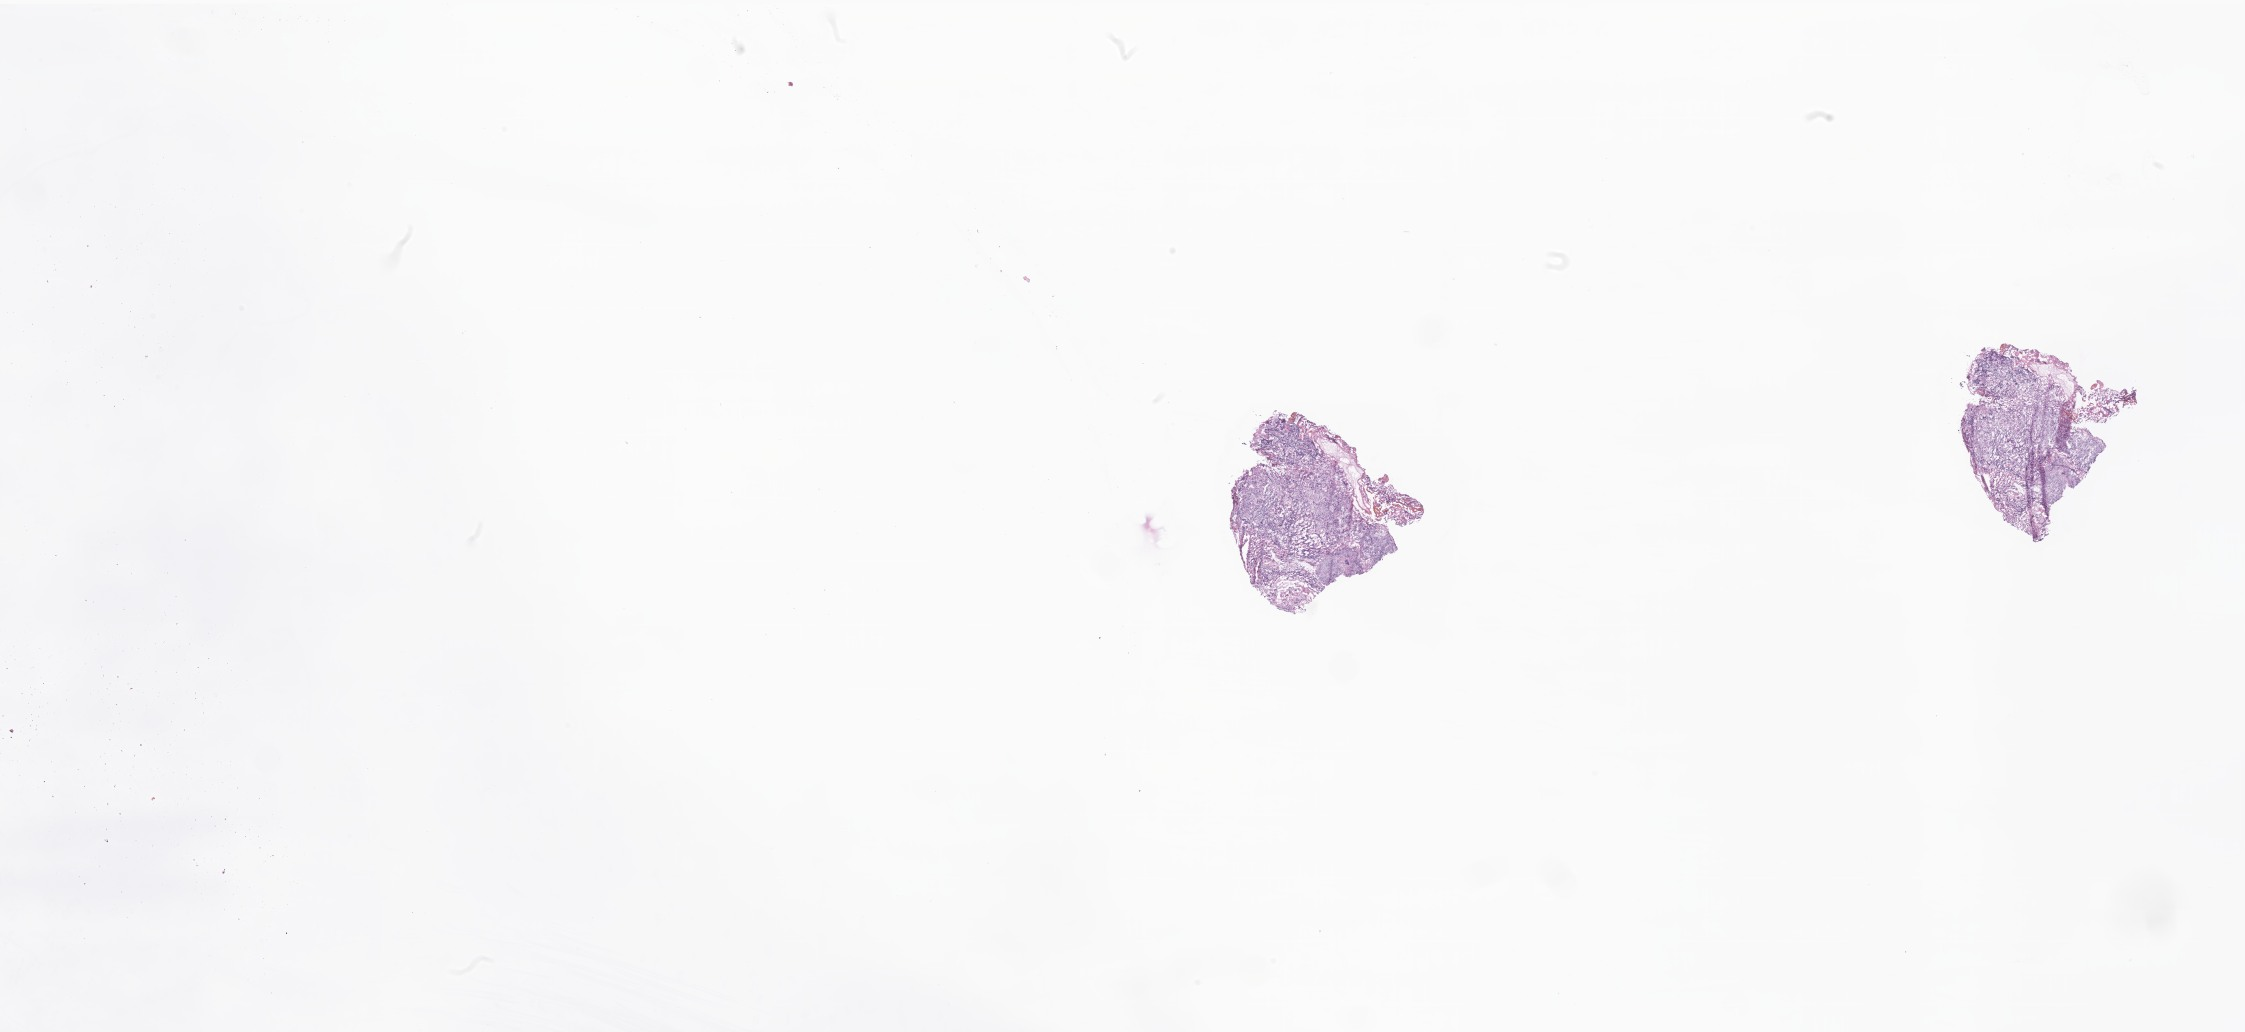
Haematoxylin and eosin whole-slide image of tumor tissue from the brain — a low-resolution overview of the entire scanned area, about 37.9 x 17.4 mm. Frozen section (OCT-embedded). Patient female; age 762 days.
* recorded diagnosis: CNS embryonal tumor, NOS